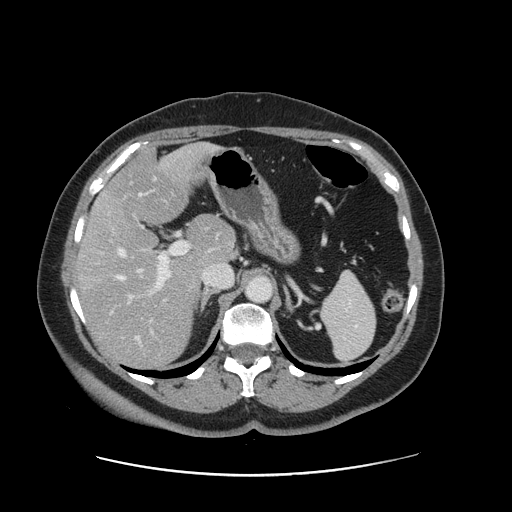
Contrast-enhanced abdominal CT, one axial slice. Position 91 of 161 along the scan axis. Soft-tissue window (W 400 / L 40 HU). 2.5 mm slice thickness. 512 × 512 image matrix, field of view 398 × 398 mm. Female patient, age 62 years. From the clinical record (not read from this slice): diagnosis: colorectal cancer liver metastases, imaged before liver resection.
Annotated regions visible in this slice (outlined manually by an expert reader):
- hepatic veins: bounding box [x1, y1, x2, y2] px = [118, 190, 153, 339]
- liver: [80, 145, 235, 367]
- planned liver remnant (the part of the liver to remain after resection): [107, 144, 235, 266]
- portal vein (with intrahepatic branches): [120, 242, 189, 339]